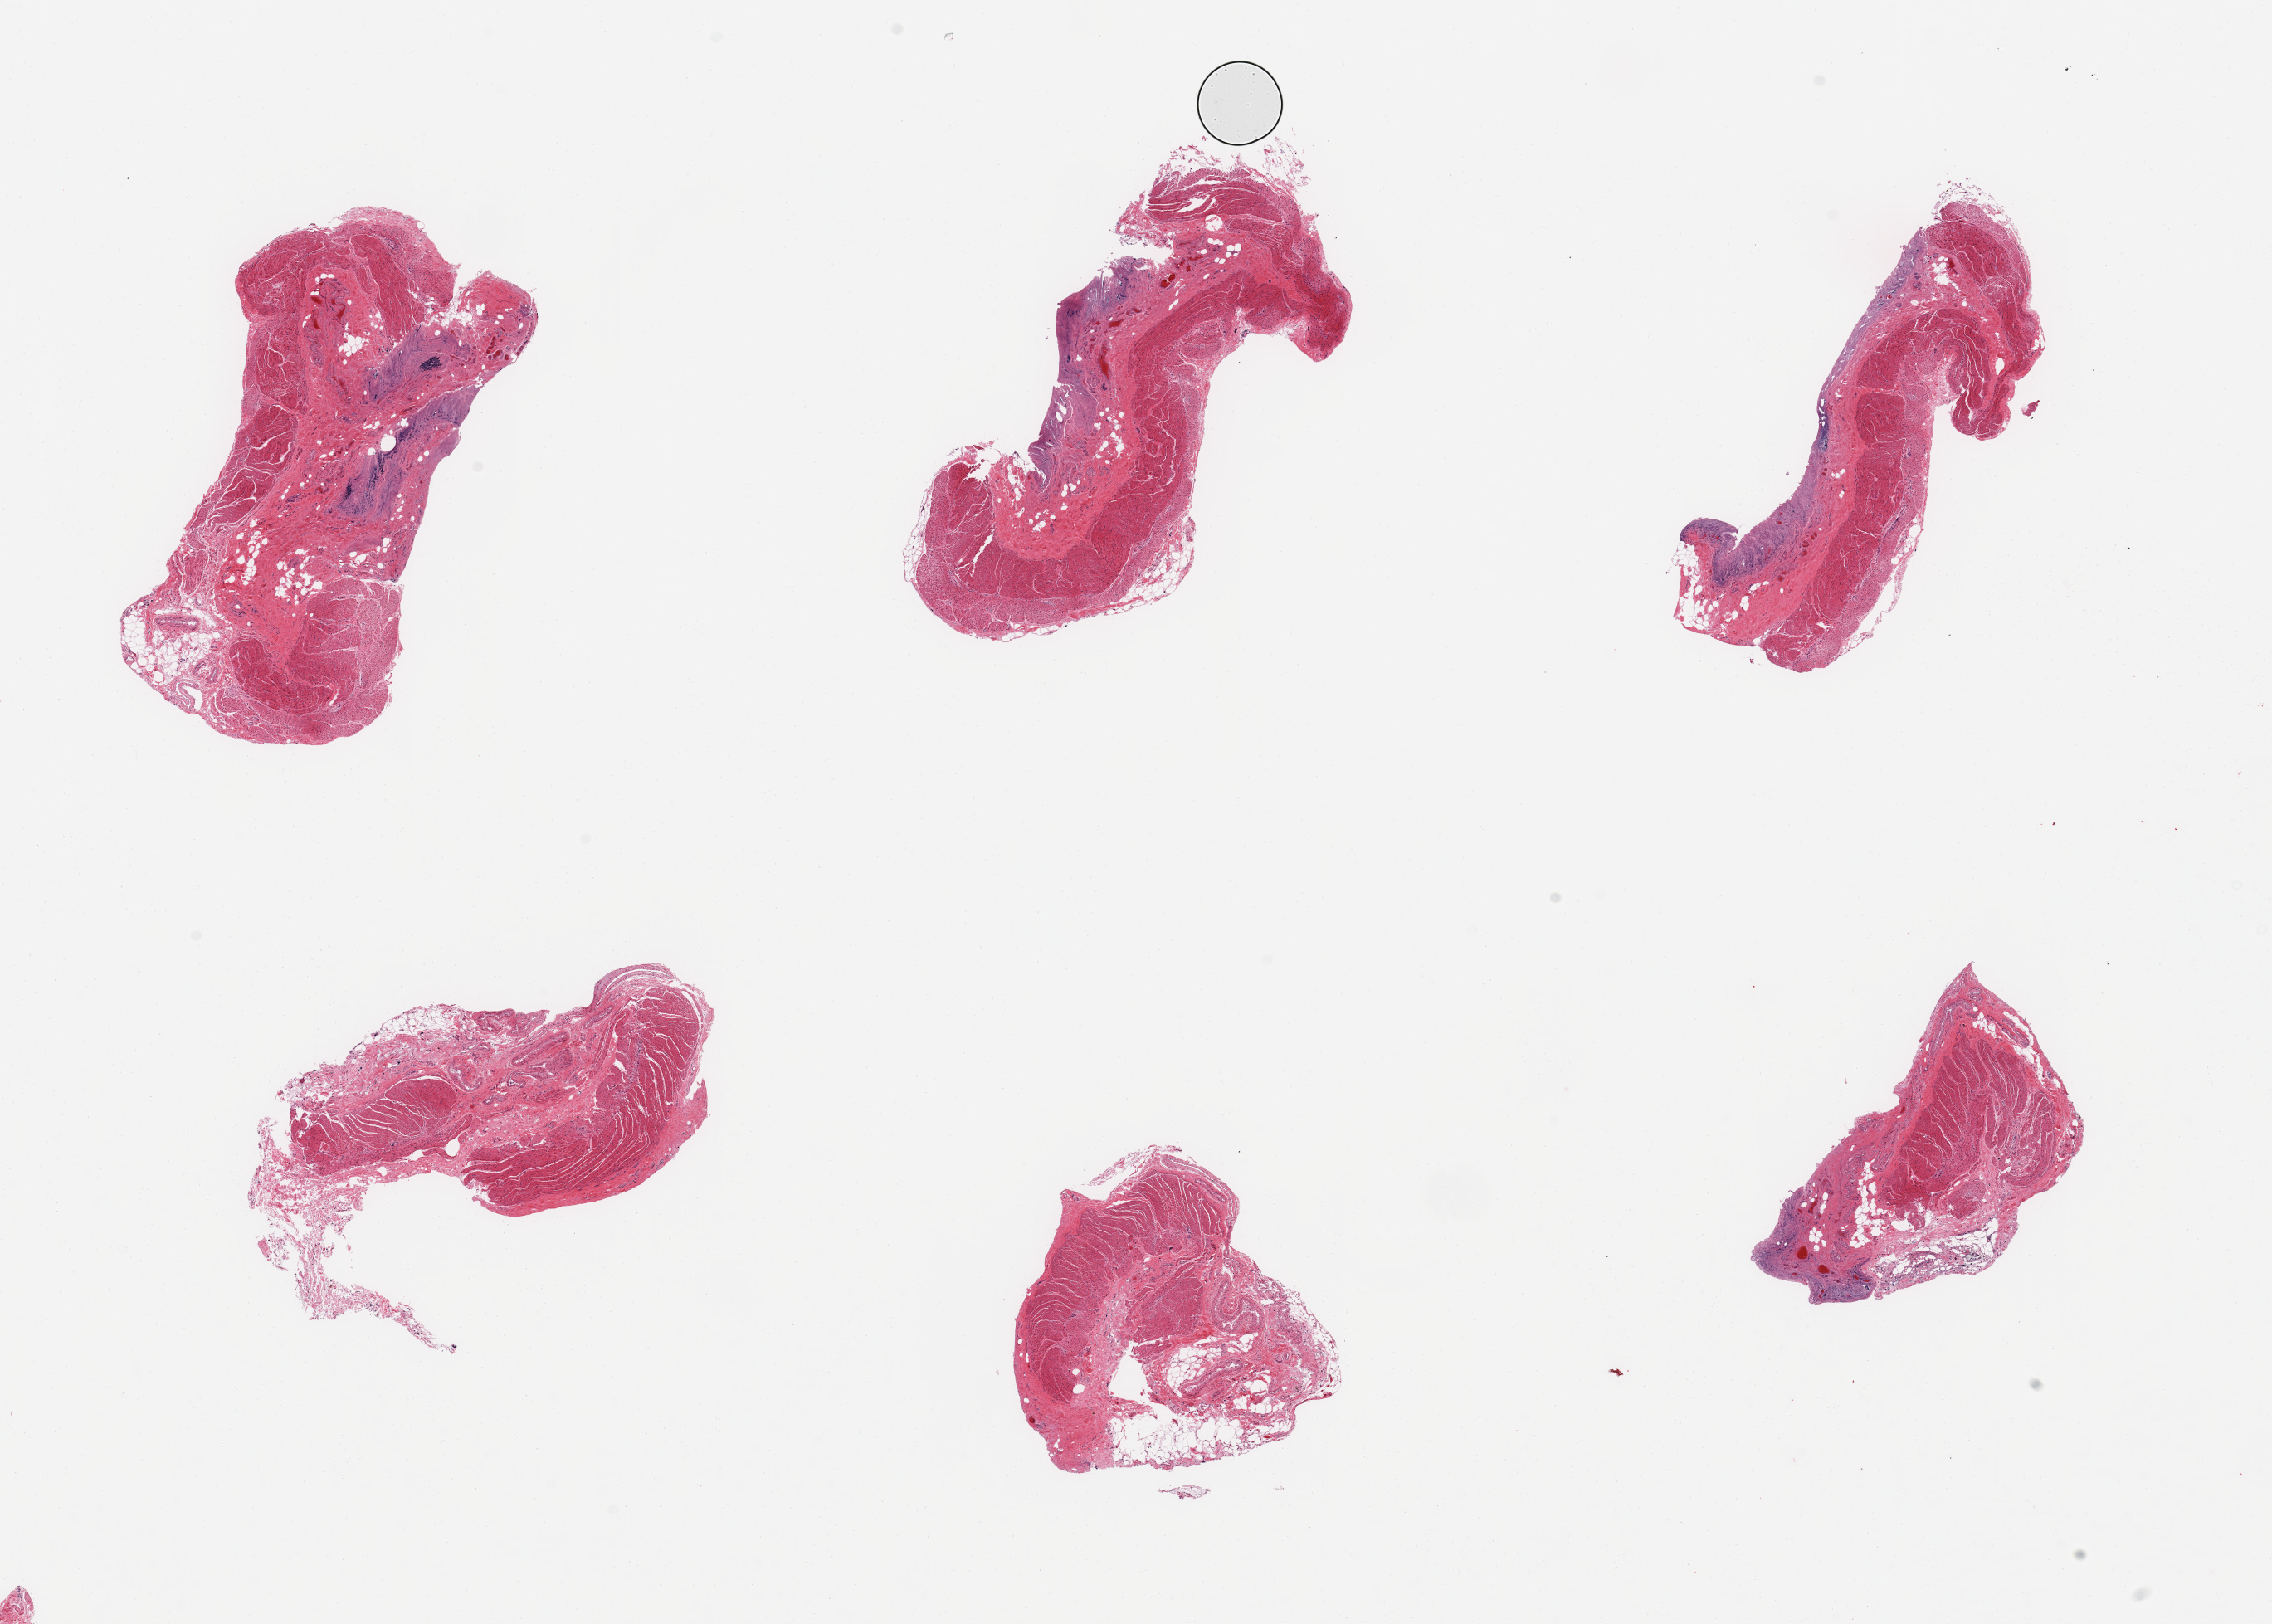
Haematoxylin and eosin whole-slide image — whole scanned area (about 21.7 x 15.5 mm, slide scanned at 20x) shown as a low-resolution overview. PAXgene-fixed, paraffin-embedded tissue. Section of transverse colon (target tissue). Donor tissue sample. Donor sex: male.
Reviewer comment on this tissue sample: 6 pieces; mucosa autolyzed, muscle intact.